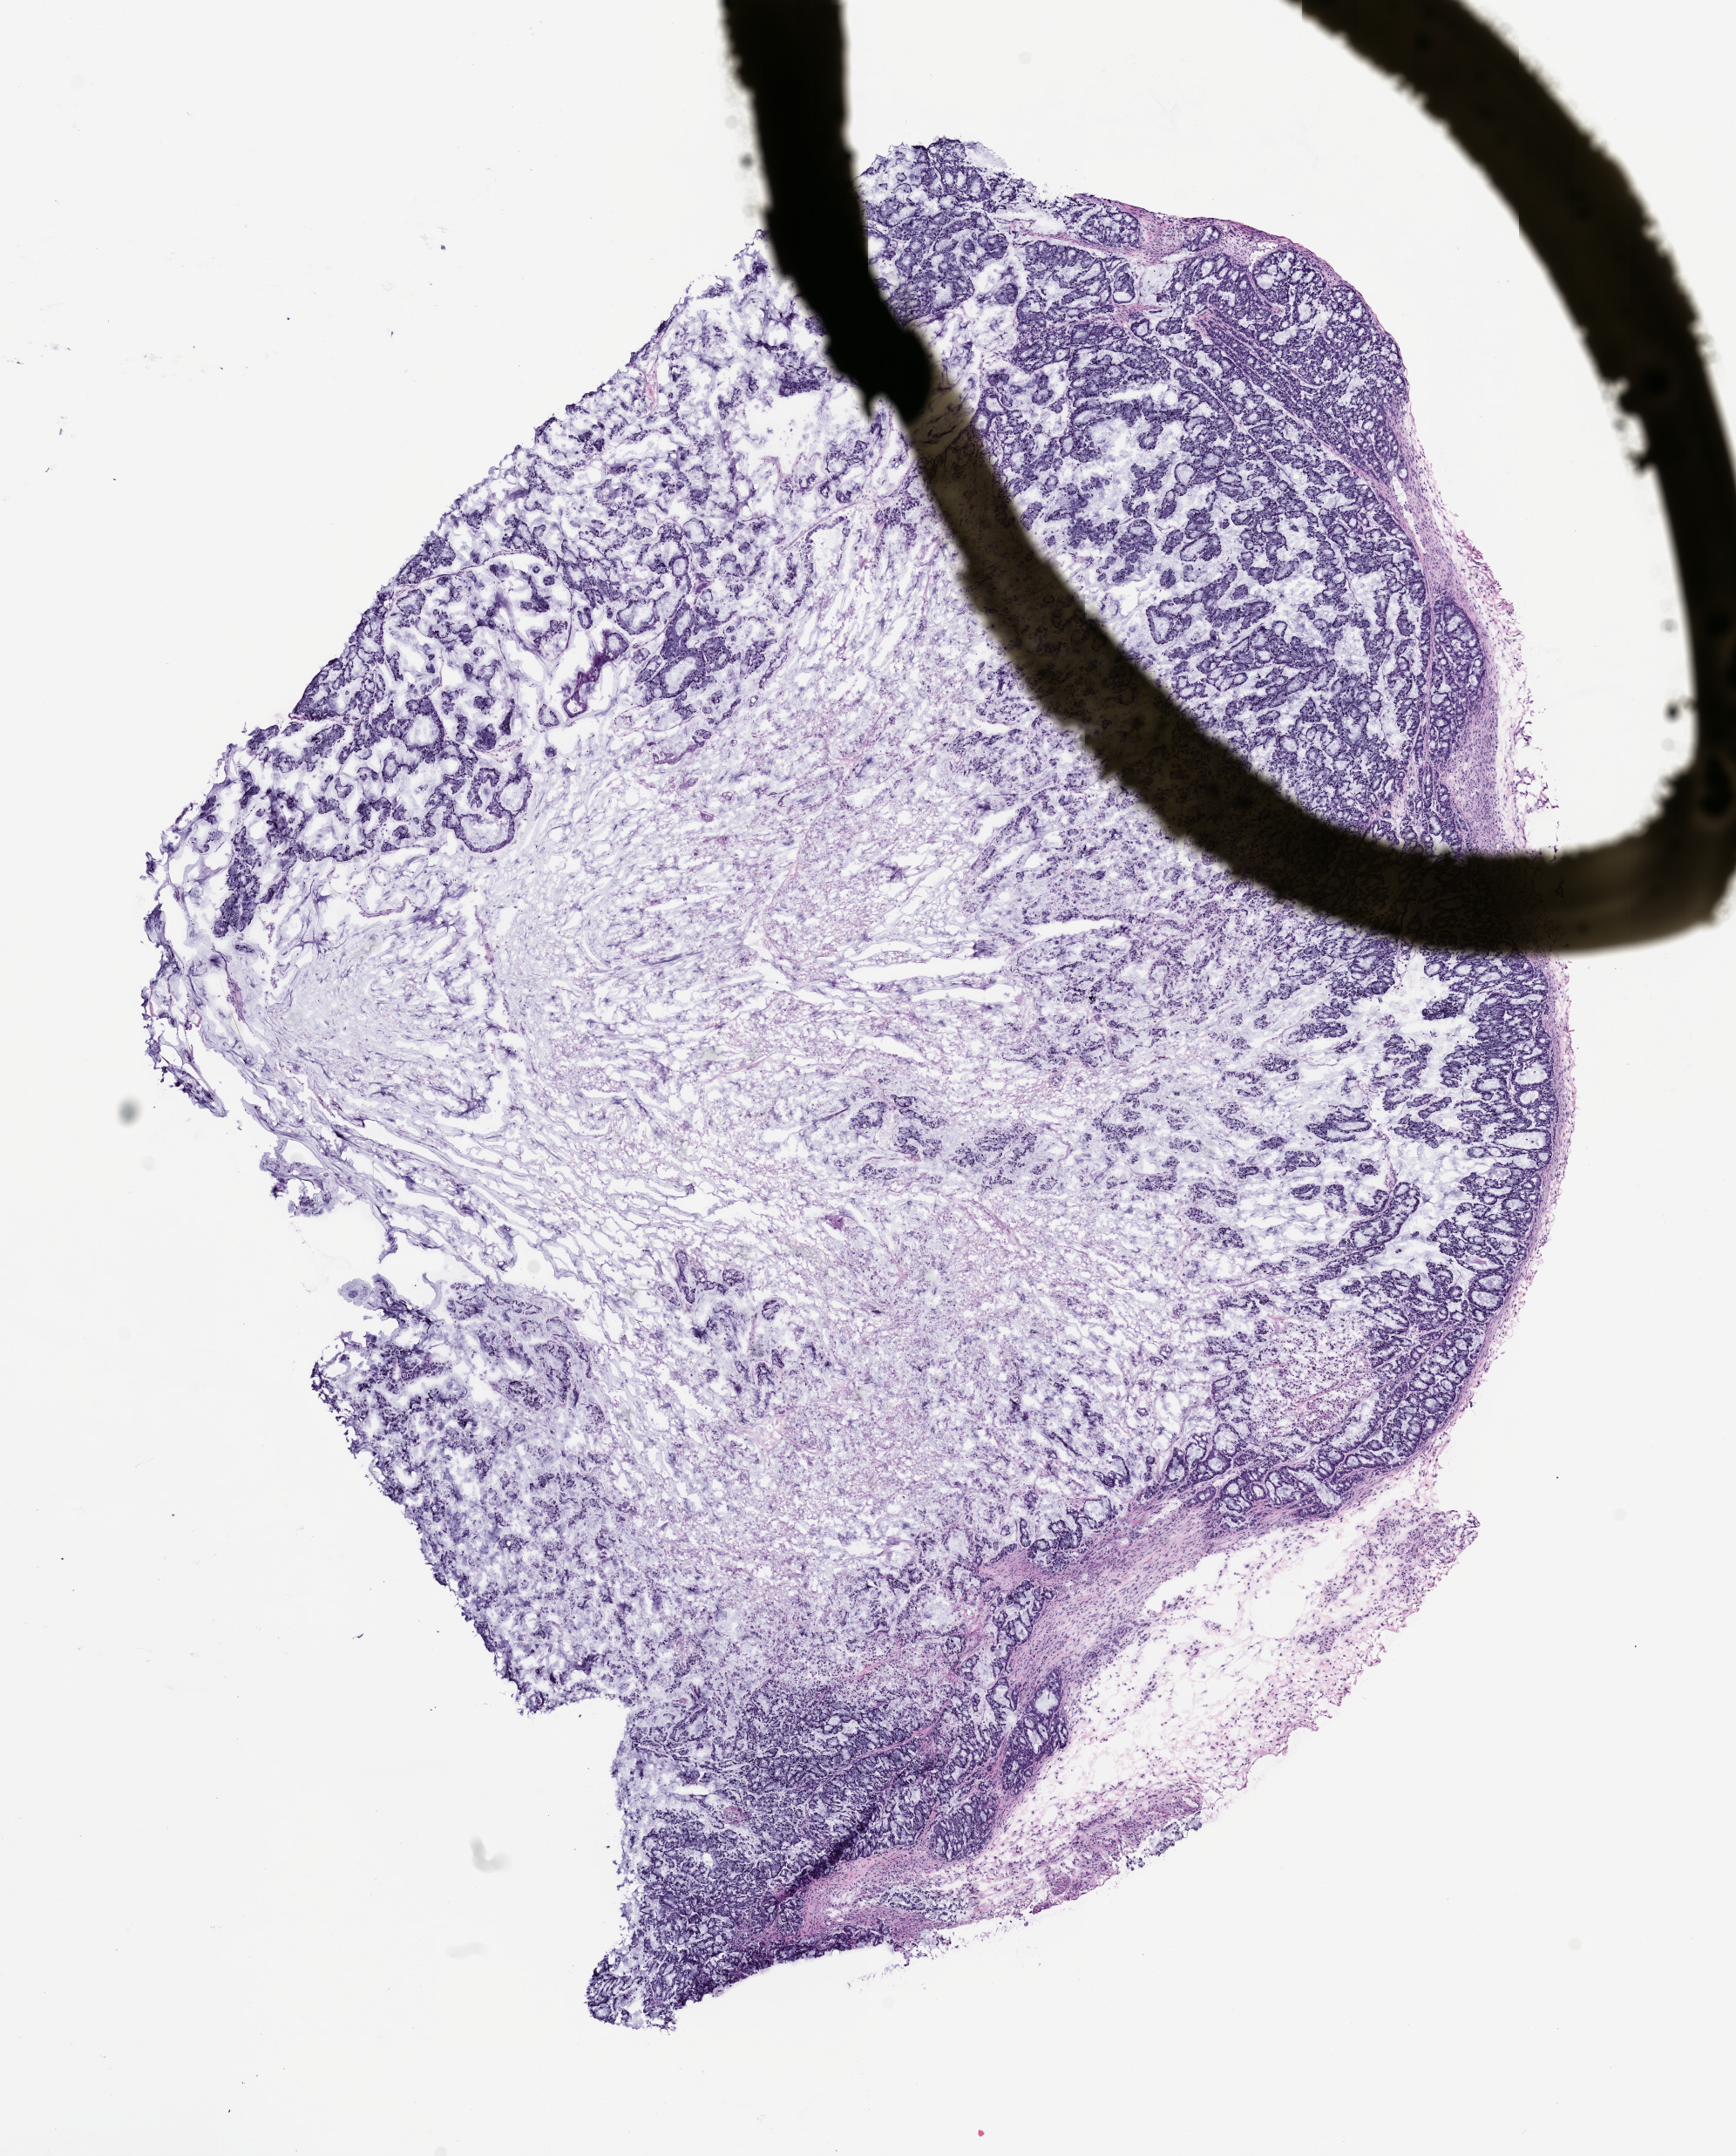
H&E whole-slide image of a patient-derived xenograft (PDX) tumor grown in a mouse, passage 2 — low-resolution overview of the scanned area, about 8.0 x 9.9 mm, FFPE section, originating tumor site category: colon.
* originating patient diagnosis: Colon Adenocarcinoma